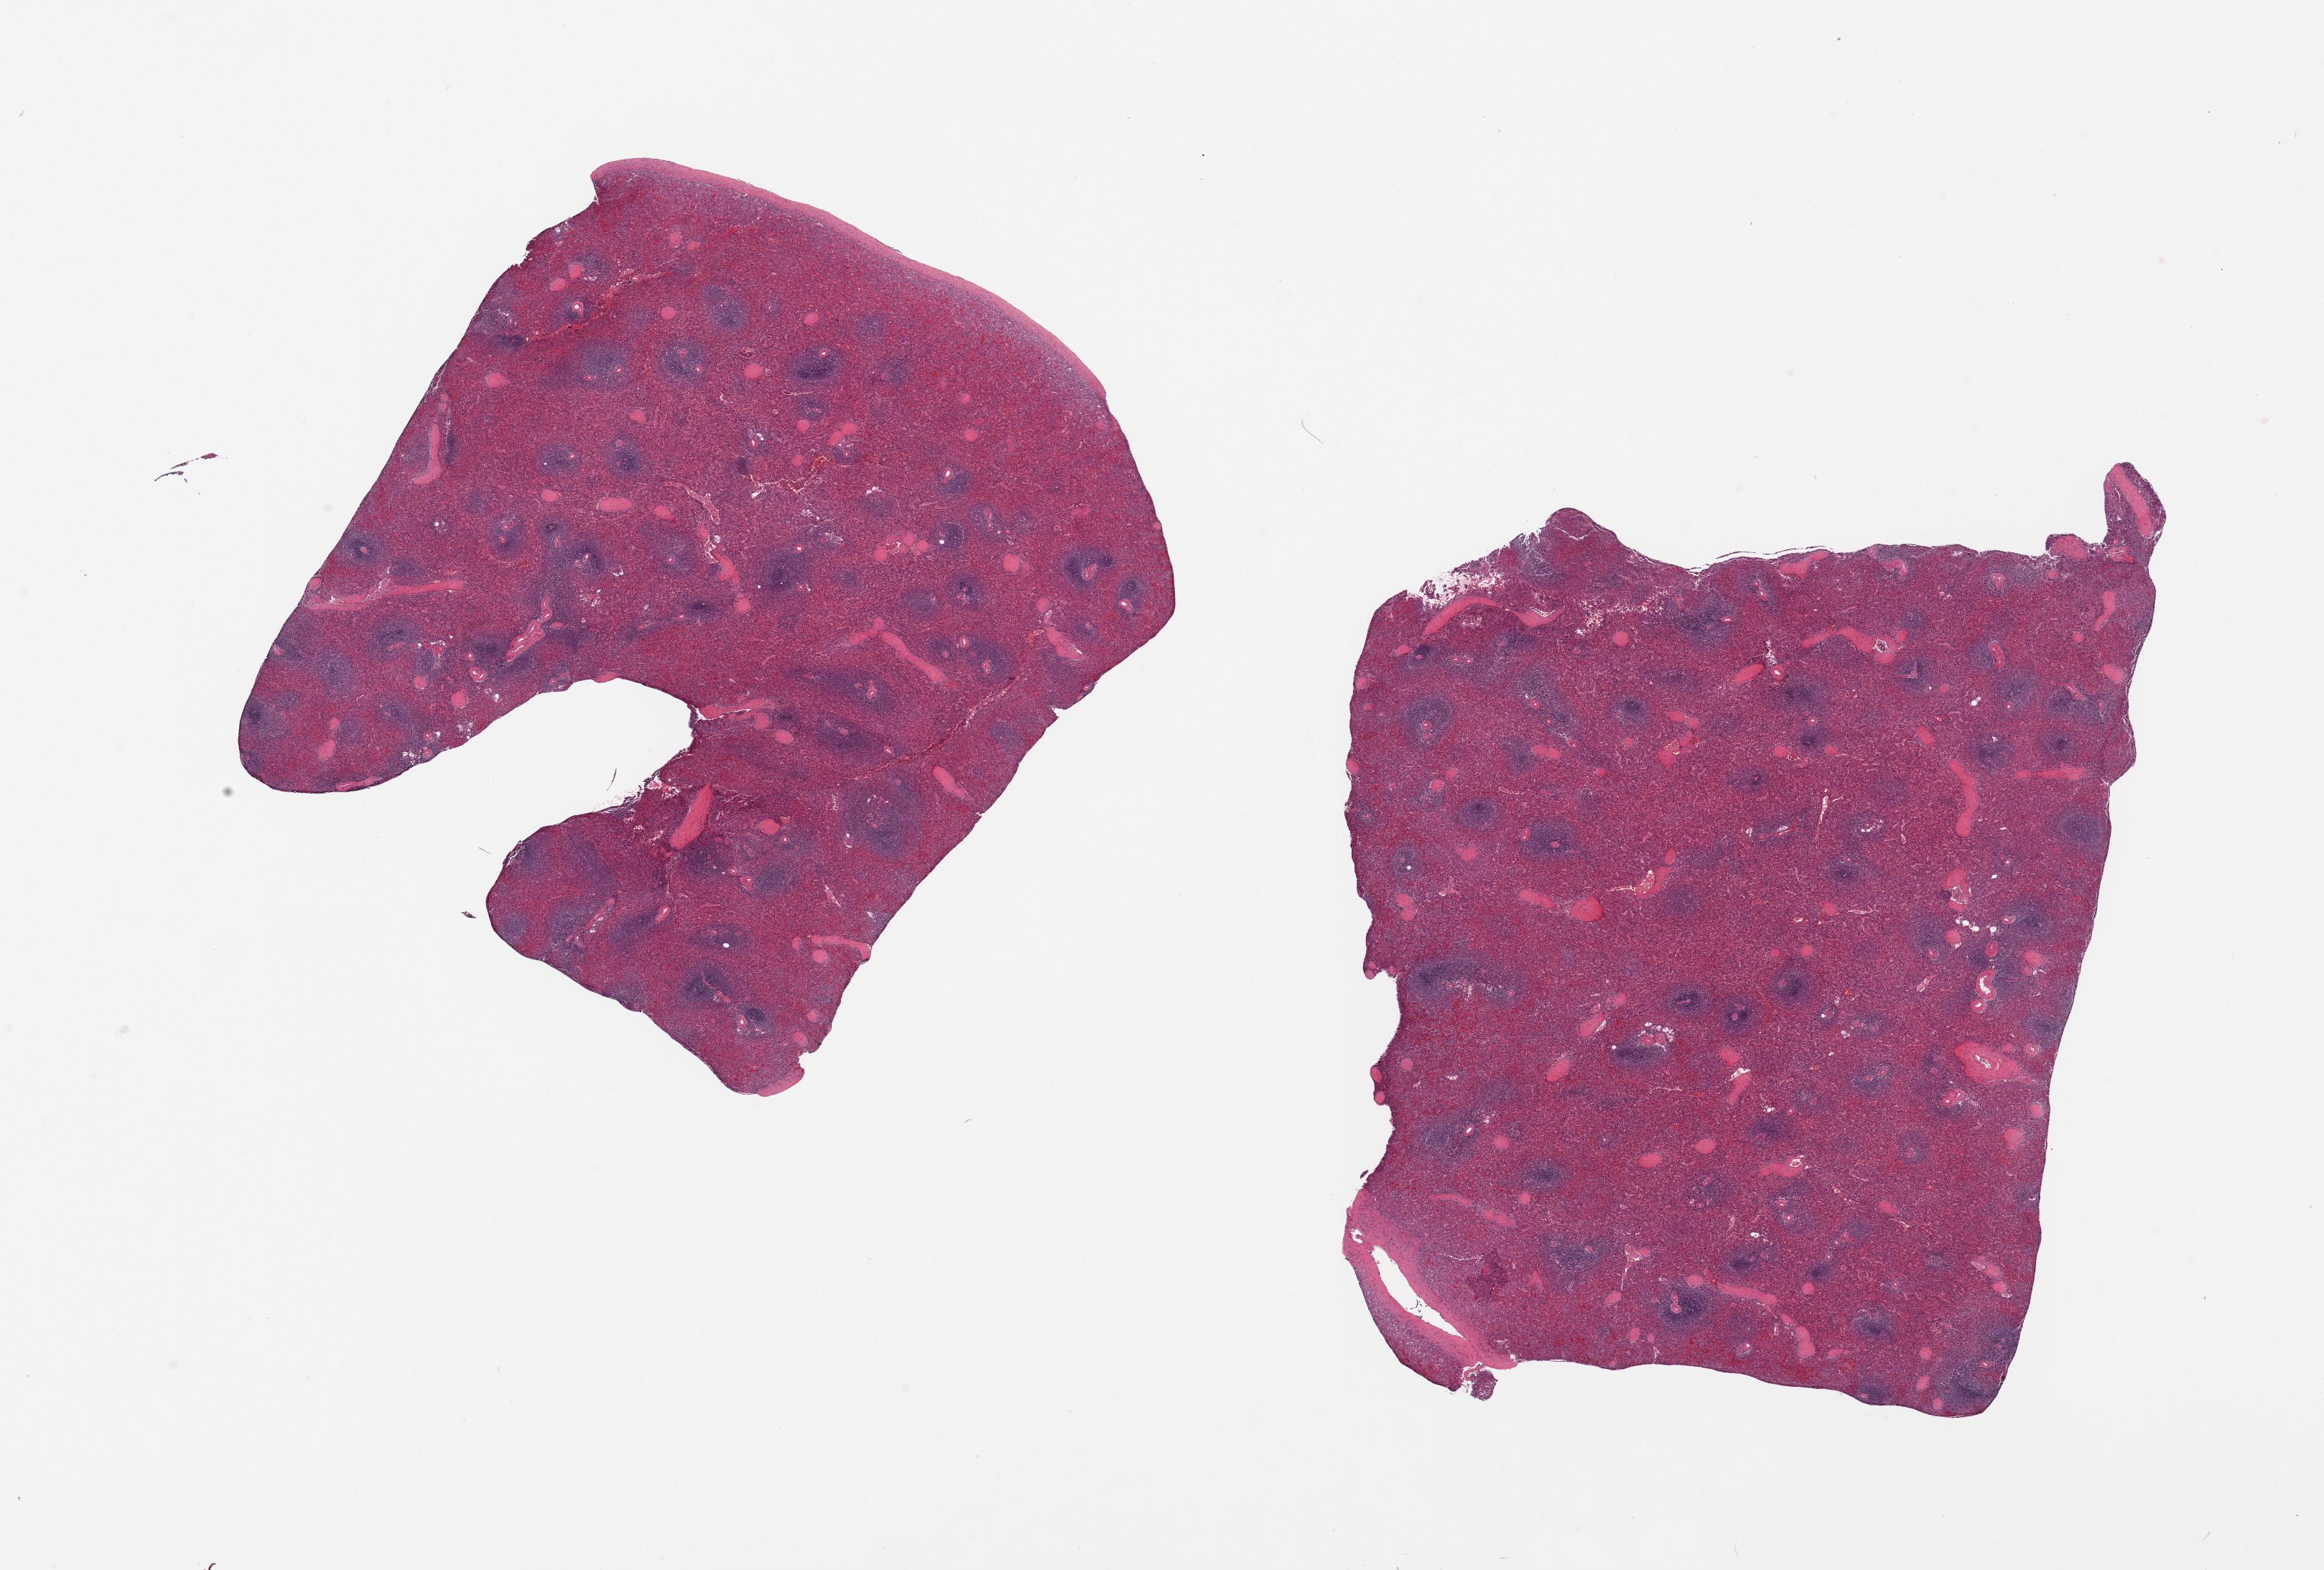
Hematoxylin and eosin (H&E) whole-slide image — low-resolution overview of the scanned area, about 25.6 x 17.3 mm (slide scanned at 20x), PAXgene-fixed, paraffin-embedded tissue, target tissue: spleen, donor tissue sample. Donor sex: male.
Review note (as recorded): 2 pieces, capsule present on one piece (should be 5mm beneath capsule).